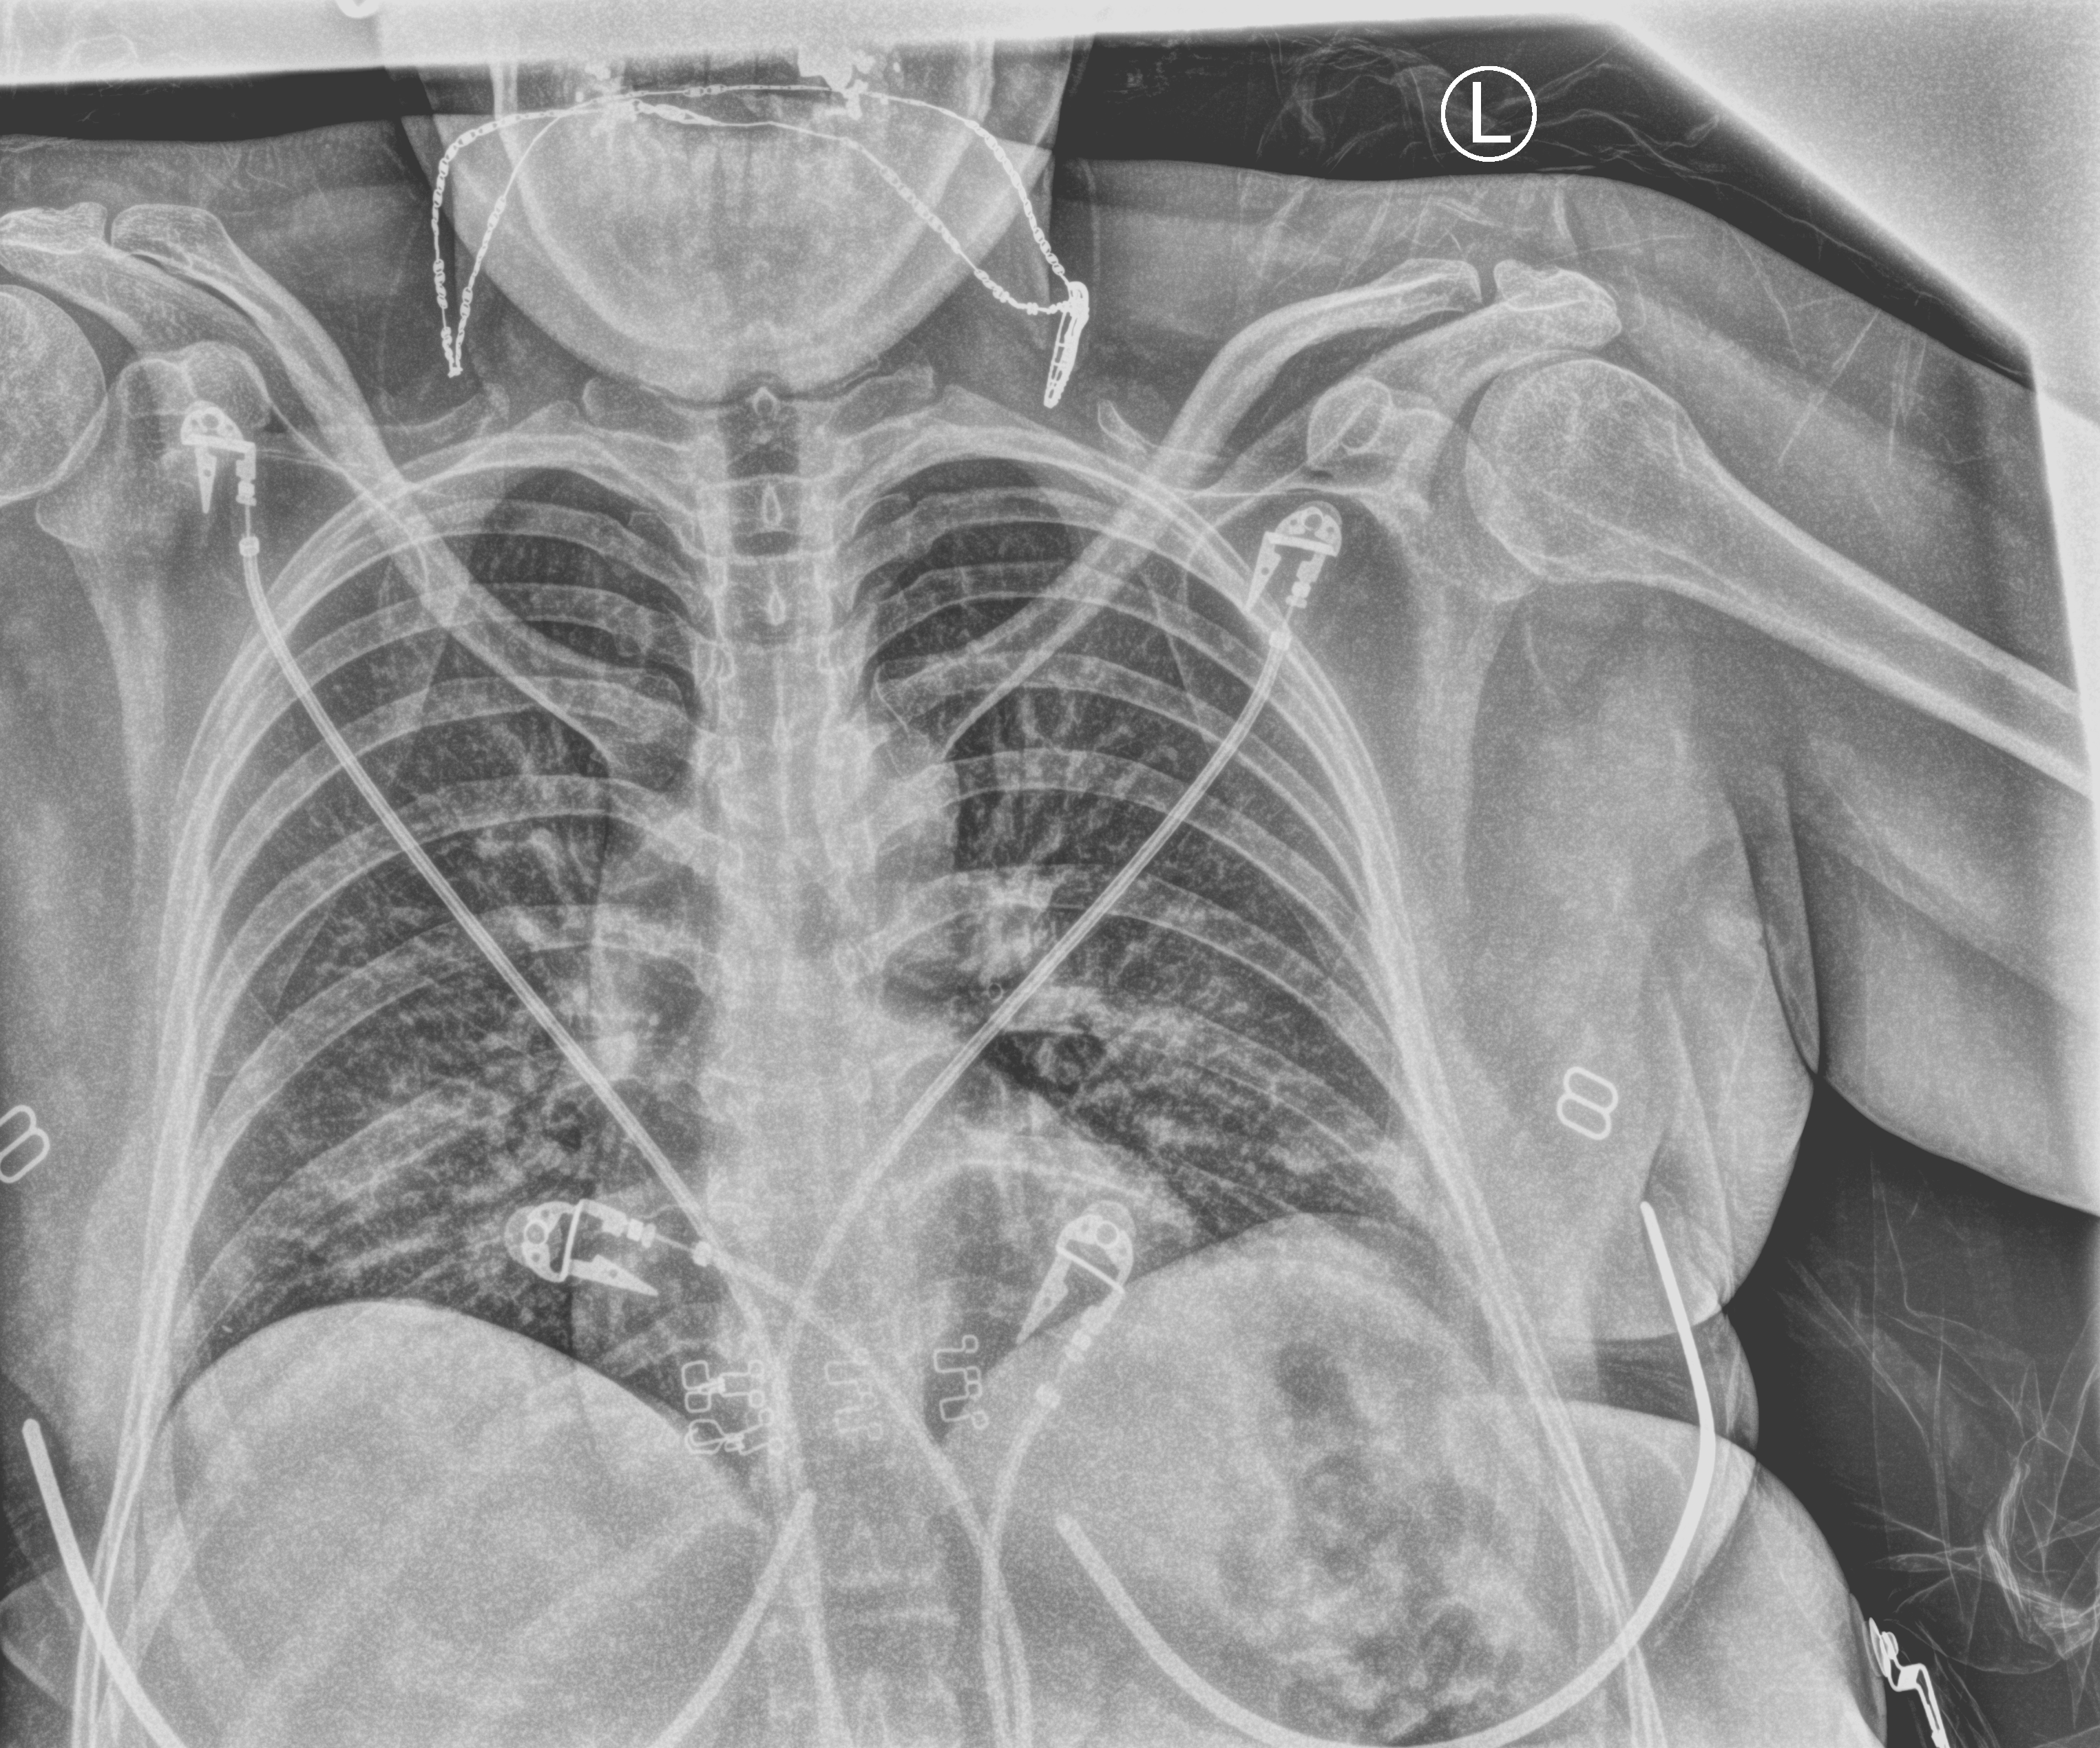
Portable chest radiograph, anteroposterior (AP) projection. Patient hospitalised with COVID-19; female, aged 18–59 years.
From the hospital-stay record, not from the radiograph (when in the stay this image was taken is not recorded):
- length of hospital stay: 1 day
- admitted to intensive care during this hospital stay: no
- mechanically ventilated during this hospital stay: no